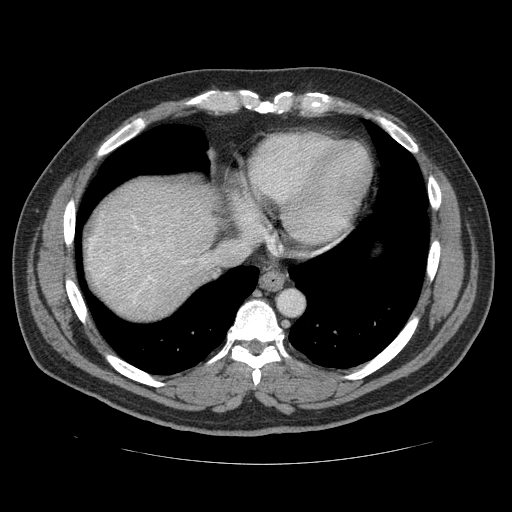
Contrast-enhanced abdominal CT (liver protocol), one axial slice. Position 106 of 113 along the scan axis. 120 kVp. Soft-tissue window (W 400 / L 40 HU). 2.5 mm slice thickness. 512 × 512 image matrix, field of view 400 × 400 mm. From the clinical record (not read from this slice): diagnosis: hepatocellular carcinoma (patient treated with transarterial chemoembolisation; whether this scan precedes or follows treatment is not stated here); TNM stage (as recorded): Stage-II; Child-Pugh class: B; tumour nodularity: multinodular.
Annotated regions visible in this slice (semi-automatically segmented with operator editing):
- abdominal aorta: bounding box (x1, y1, x2, y2) in pixels: (279, 291, 302, 315)
- liver parenchyma outside the tumour (the mass and vessels are separate outlines, so this box may not span the whole liver): (84, 176, 214, 314)
- liver vessels: (140, 229, 157, 252)